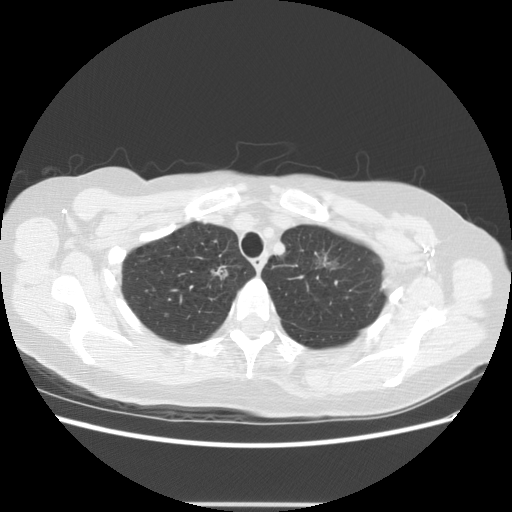
Low-dose screening chest CT, one axial slice; slice 106 of 126 in the series (ordered by position); reconstruction kernel STANDARD; 140 kVp; lung window (W 1500 / L -600 HU); 2.5 mm slice thickness; 512 × 512 image matrix, field of view 360 × 360 mm.
Structures marked on this image (expert manual segmentation):
- lesion 1 (tumor, upper lobe of right lung): box from (x=211, y=266) to (x=229, y=280) px